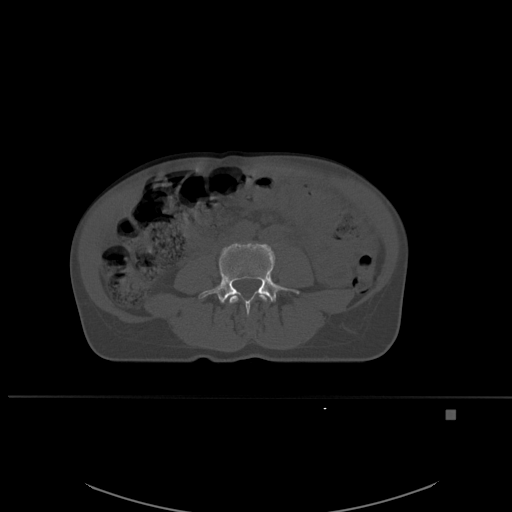
CT including the spine, one axial slice. Slice 197 of 537 in the series (ordered by position). Bone window (W 1800 / L 400 HU). 512 × 512 image matrix, field of view 440 × 440 mm. Patient: female, 45 years. Case-level facts recorded for this patient, not image findings: primary cancer: lung.
Annotated regions visible in this slice (semi-automatic segmentation, software-assisted and operator-edited):
- L3 vertebra: bounding box (x1, y1, x2, y2) in pixels: (229, 293, 268, 304)
- L4 vertebra: (198, 243, 299, 315)